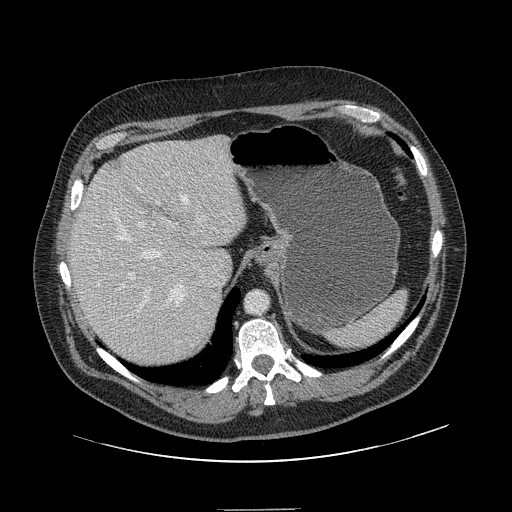
Contrast-enhanced abdominal CT, one axial slice; position 111 of 154 along the scan axis; 120 kVp; intravenous contrast given; soft-tissue window (W 400 / L 40 HU); 2.5 mm slice thickness; 512 × 512 image matrix. Male patient, age 61 years. Case-level facts recorded for this patient, not image findings: diagnosis: colorectal cancer liver metastases, imaged before liver resection; multiple liver metastases: yes; largest metastasis: 2.6 cm; disease in both lobes: yes.
Outlined on this slice (manually delineated by an expert):
- hepatic veins: bounding box (x1, y1, x2, y2) in pixels: (113, 195, 188, 306)
- liver: (71, 137, 245, 367)
- planned liver remnant (the part of the liver to remain after resection): (71, 144, 245, 358)
- portal vein (with intrahepatic branches): (121, 201, 206, 315)